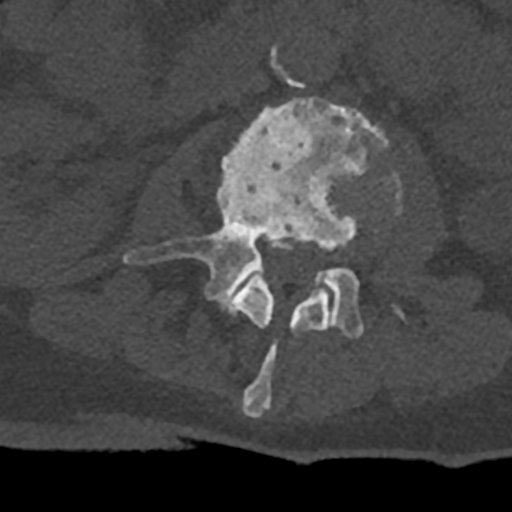
CT including the spine, one axial slice. Slice 343 of 797 in the series (ordered by position). Reconstruction kernel Br40s/3. 120 kVp. Bone window (W 1800 / L 400 HU). 512 × 512 image matrix, field of view 160 × 160 mm. Male patient, age 74 years. Case-level facts recorded for this patient, not image findings: primary cancer: renal; vertebrae with lytic lesions (as recorded): T10, L1, L2, L3, L4, L5.
Outlined on this slice (semi-automatic segmentation, software-assisted and operator-edited):
- L2 vertebra: box from (x=227, y=266) to (x=331, y=417) px
- L3 vertebra: (x=123, y=97)–(x=402, y=339)